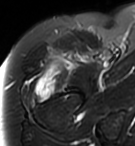
MRI of an extremity soft-tissue mass, one axial slice; position 82 of 95 along the scan axis; T2-weighted fat-saturated; MR volume resampled by the dataset authors to the PET/CT grid (not the native acquisition matrix); 3.27 mm slice thickness; 135 × 146 image matrix, field of view 132 × 143 mm. Female patient. Case-level facts recorded for this patient, not image findings: histological type: pleiomorphic undifferentiated sarcoma; grade: high; site of the primary tumour: right quadricep.
Outlined on this slice (expert contour drawn on MRI and transferred to this co-registered scan by the dataset authors):
- gross tumour volume including surrounding oedema: bounding box <30,65,81,103> (left, top, right, bottom; pixels)